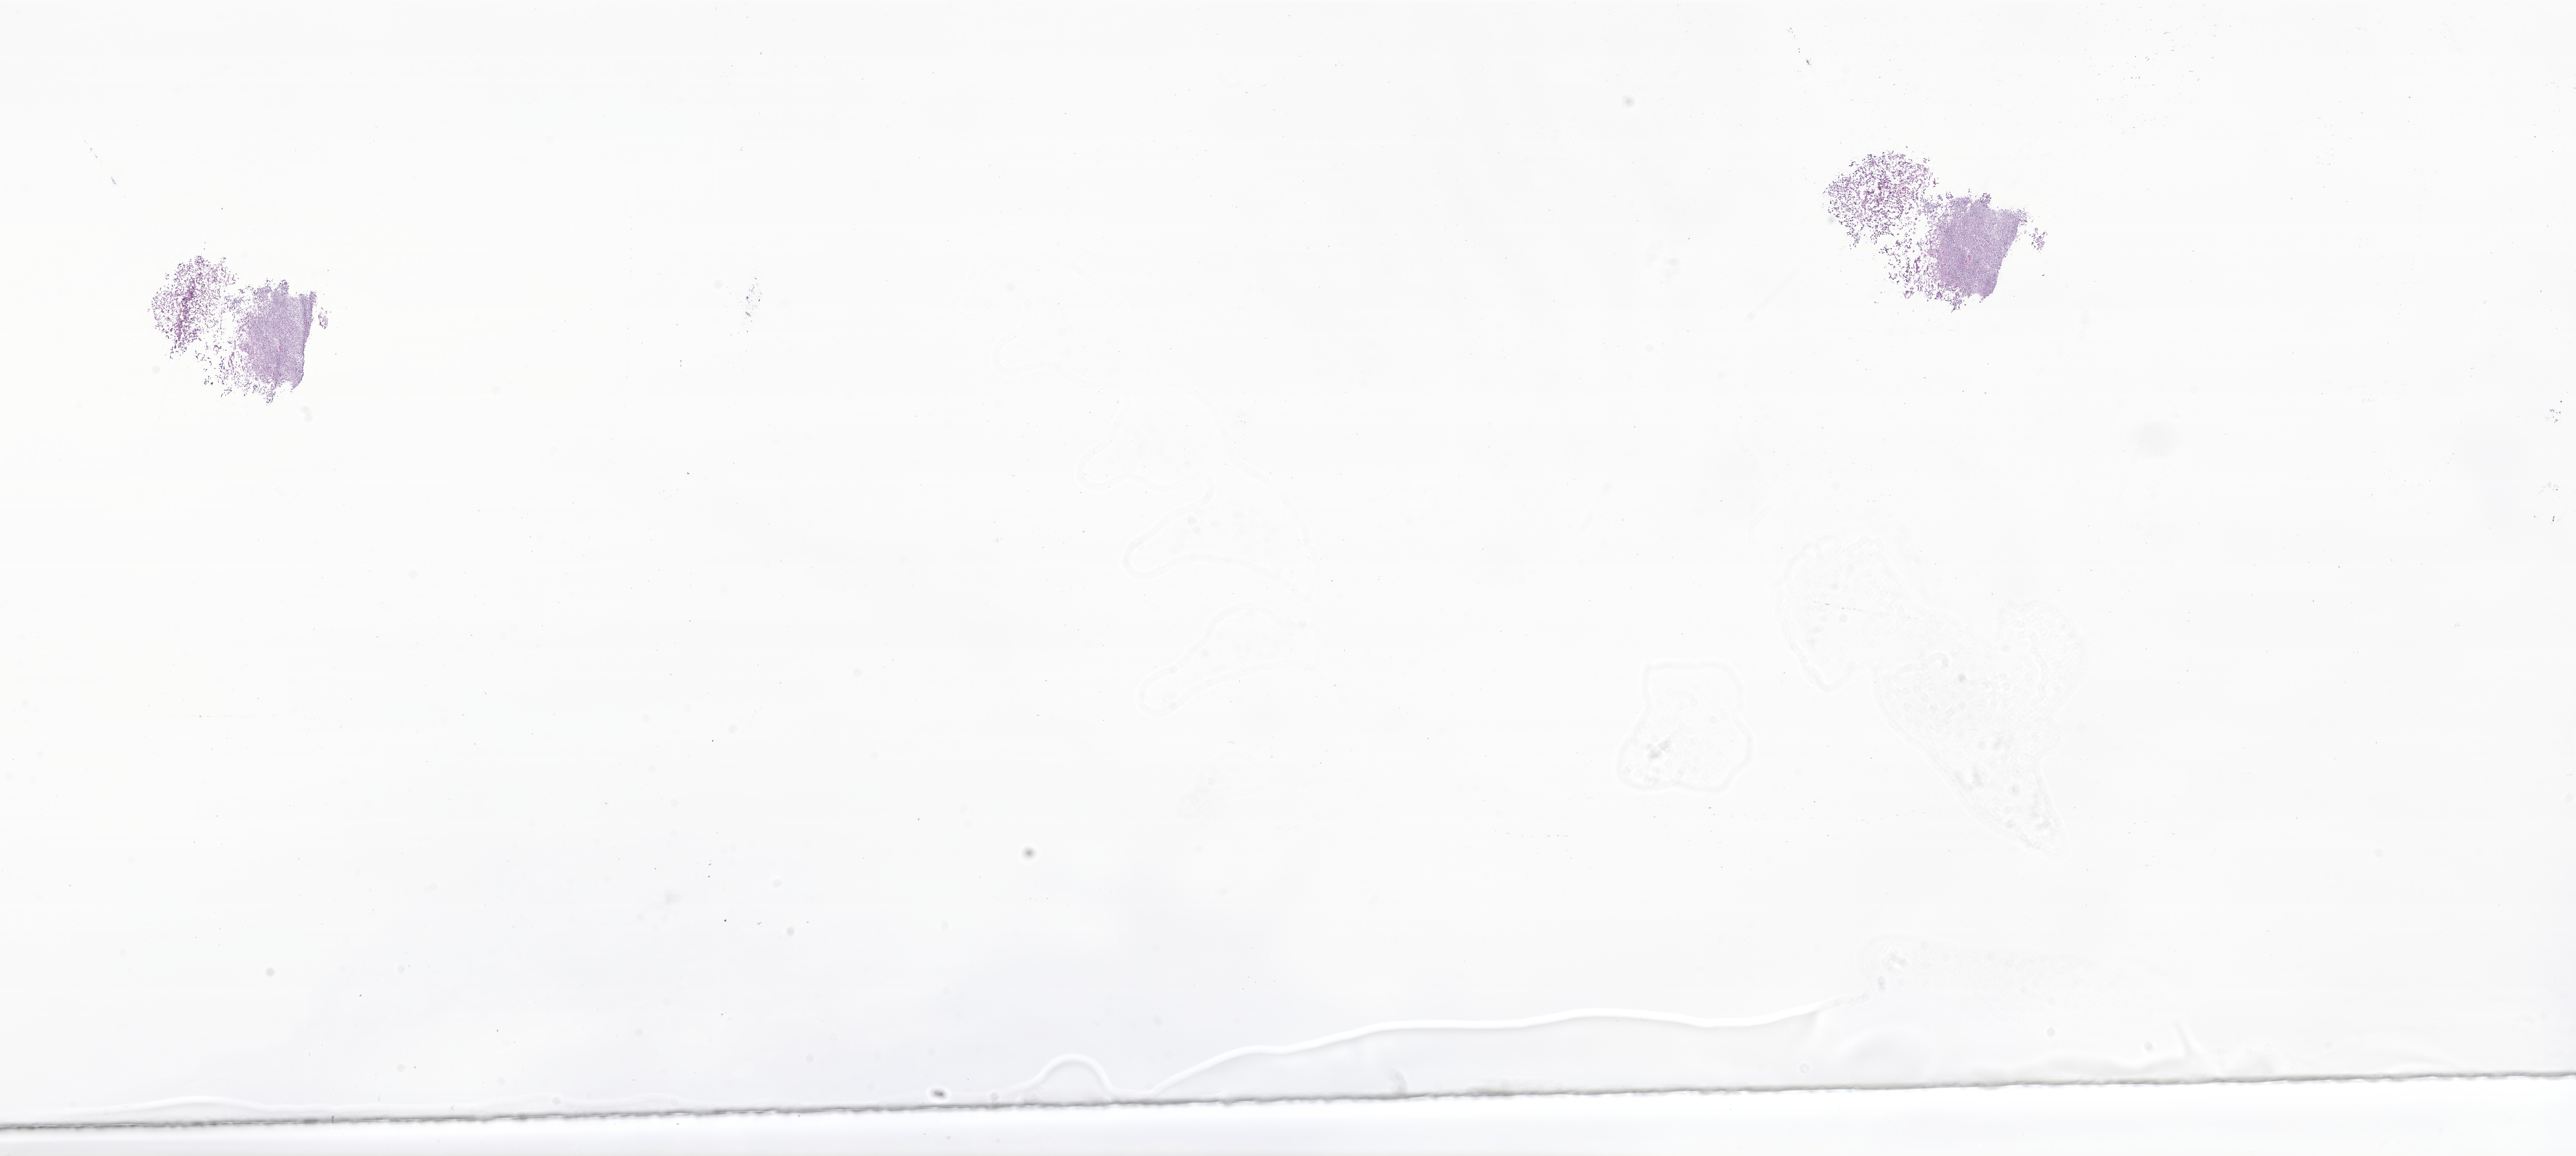
Whole-slide image, haematoxylin and eosin stain of tumor tissue from the brain, a low-resolution overview of the entire scanned area, about 32.4 x 14.5 mm; cryosection (OCT / tissue freezing medium). Patient: female, age 160 months.
Diagnosis: Tumor cells, uncertain whether benign or malignant.